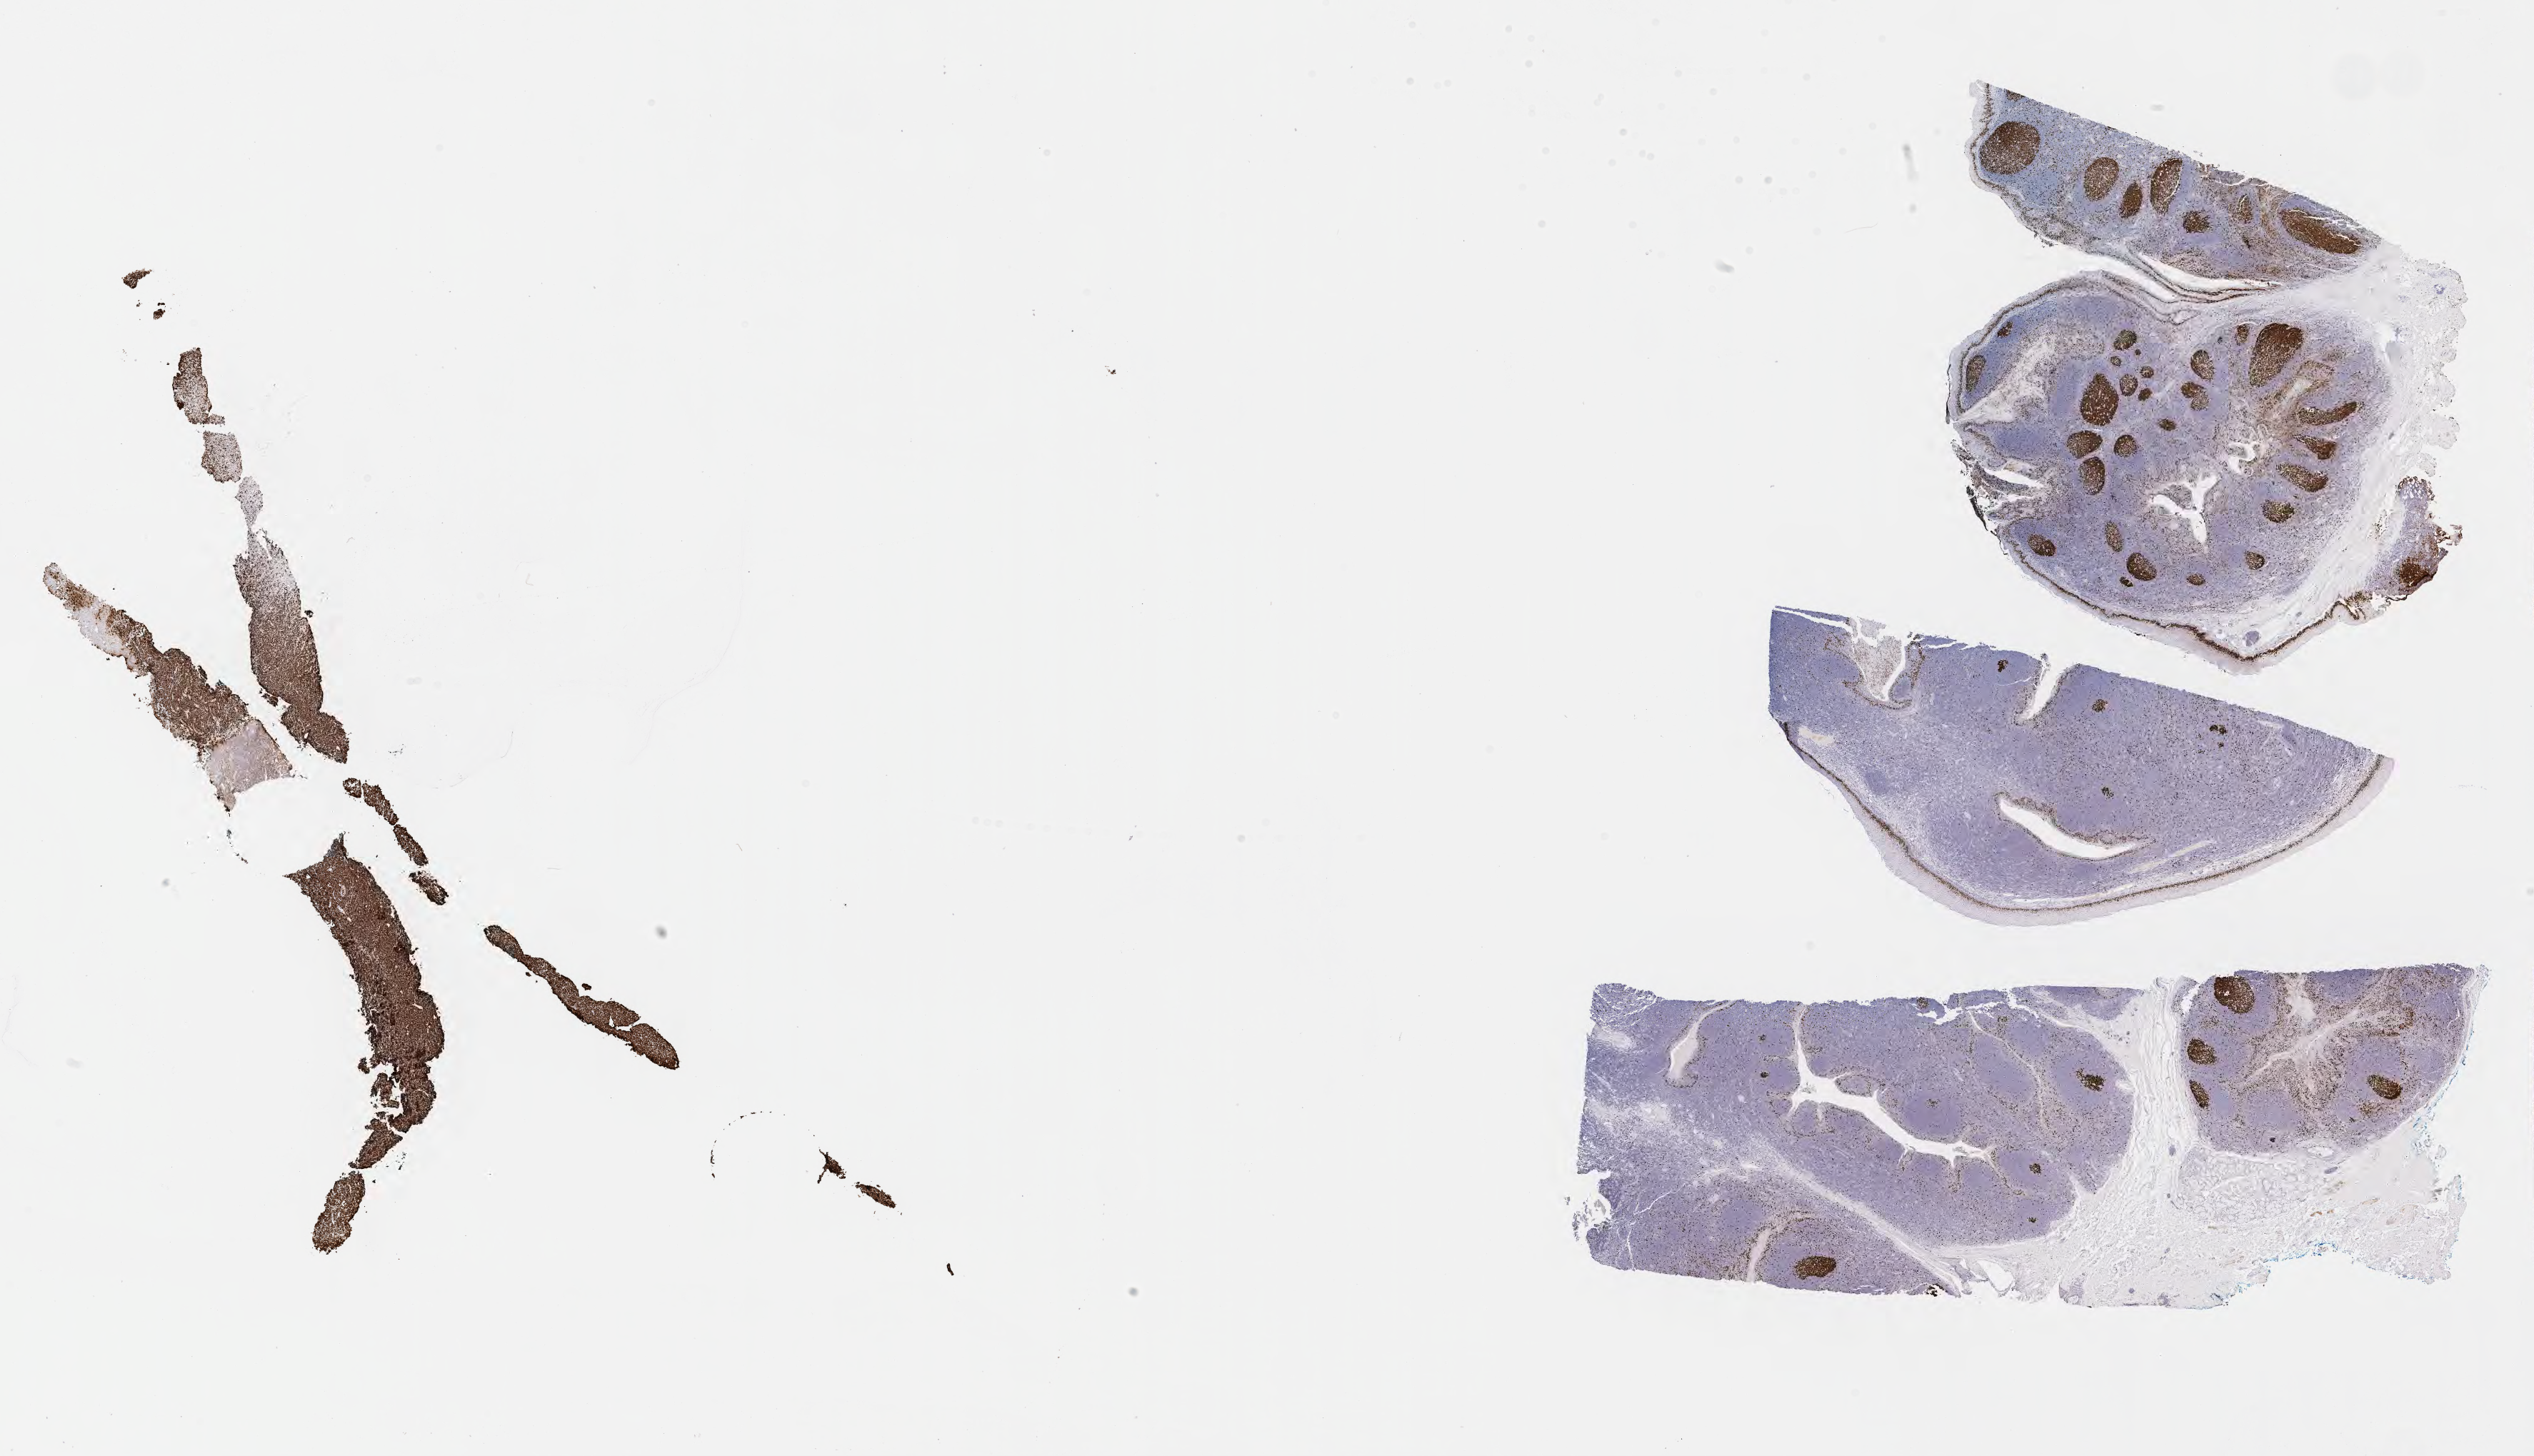
Immunohistochemistry (IHC) whole-slide image stained for Ki-67, shown as a low-resolution overview of the whole scanned area (about 28.7 x 16.5 mm). Tumor tissue. Anatomic site: abdomen proper. Patient male; age 14 years.
• histologic diagnosis: Burkitt lymphoma, NOS